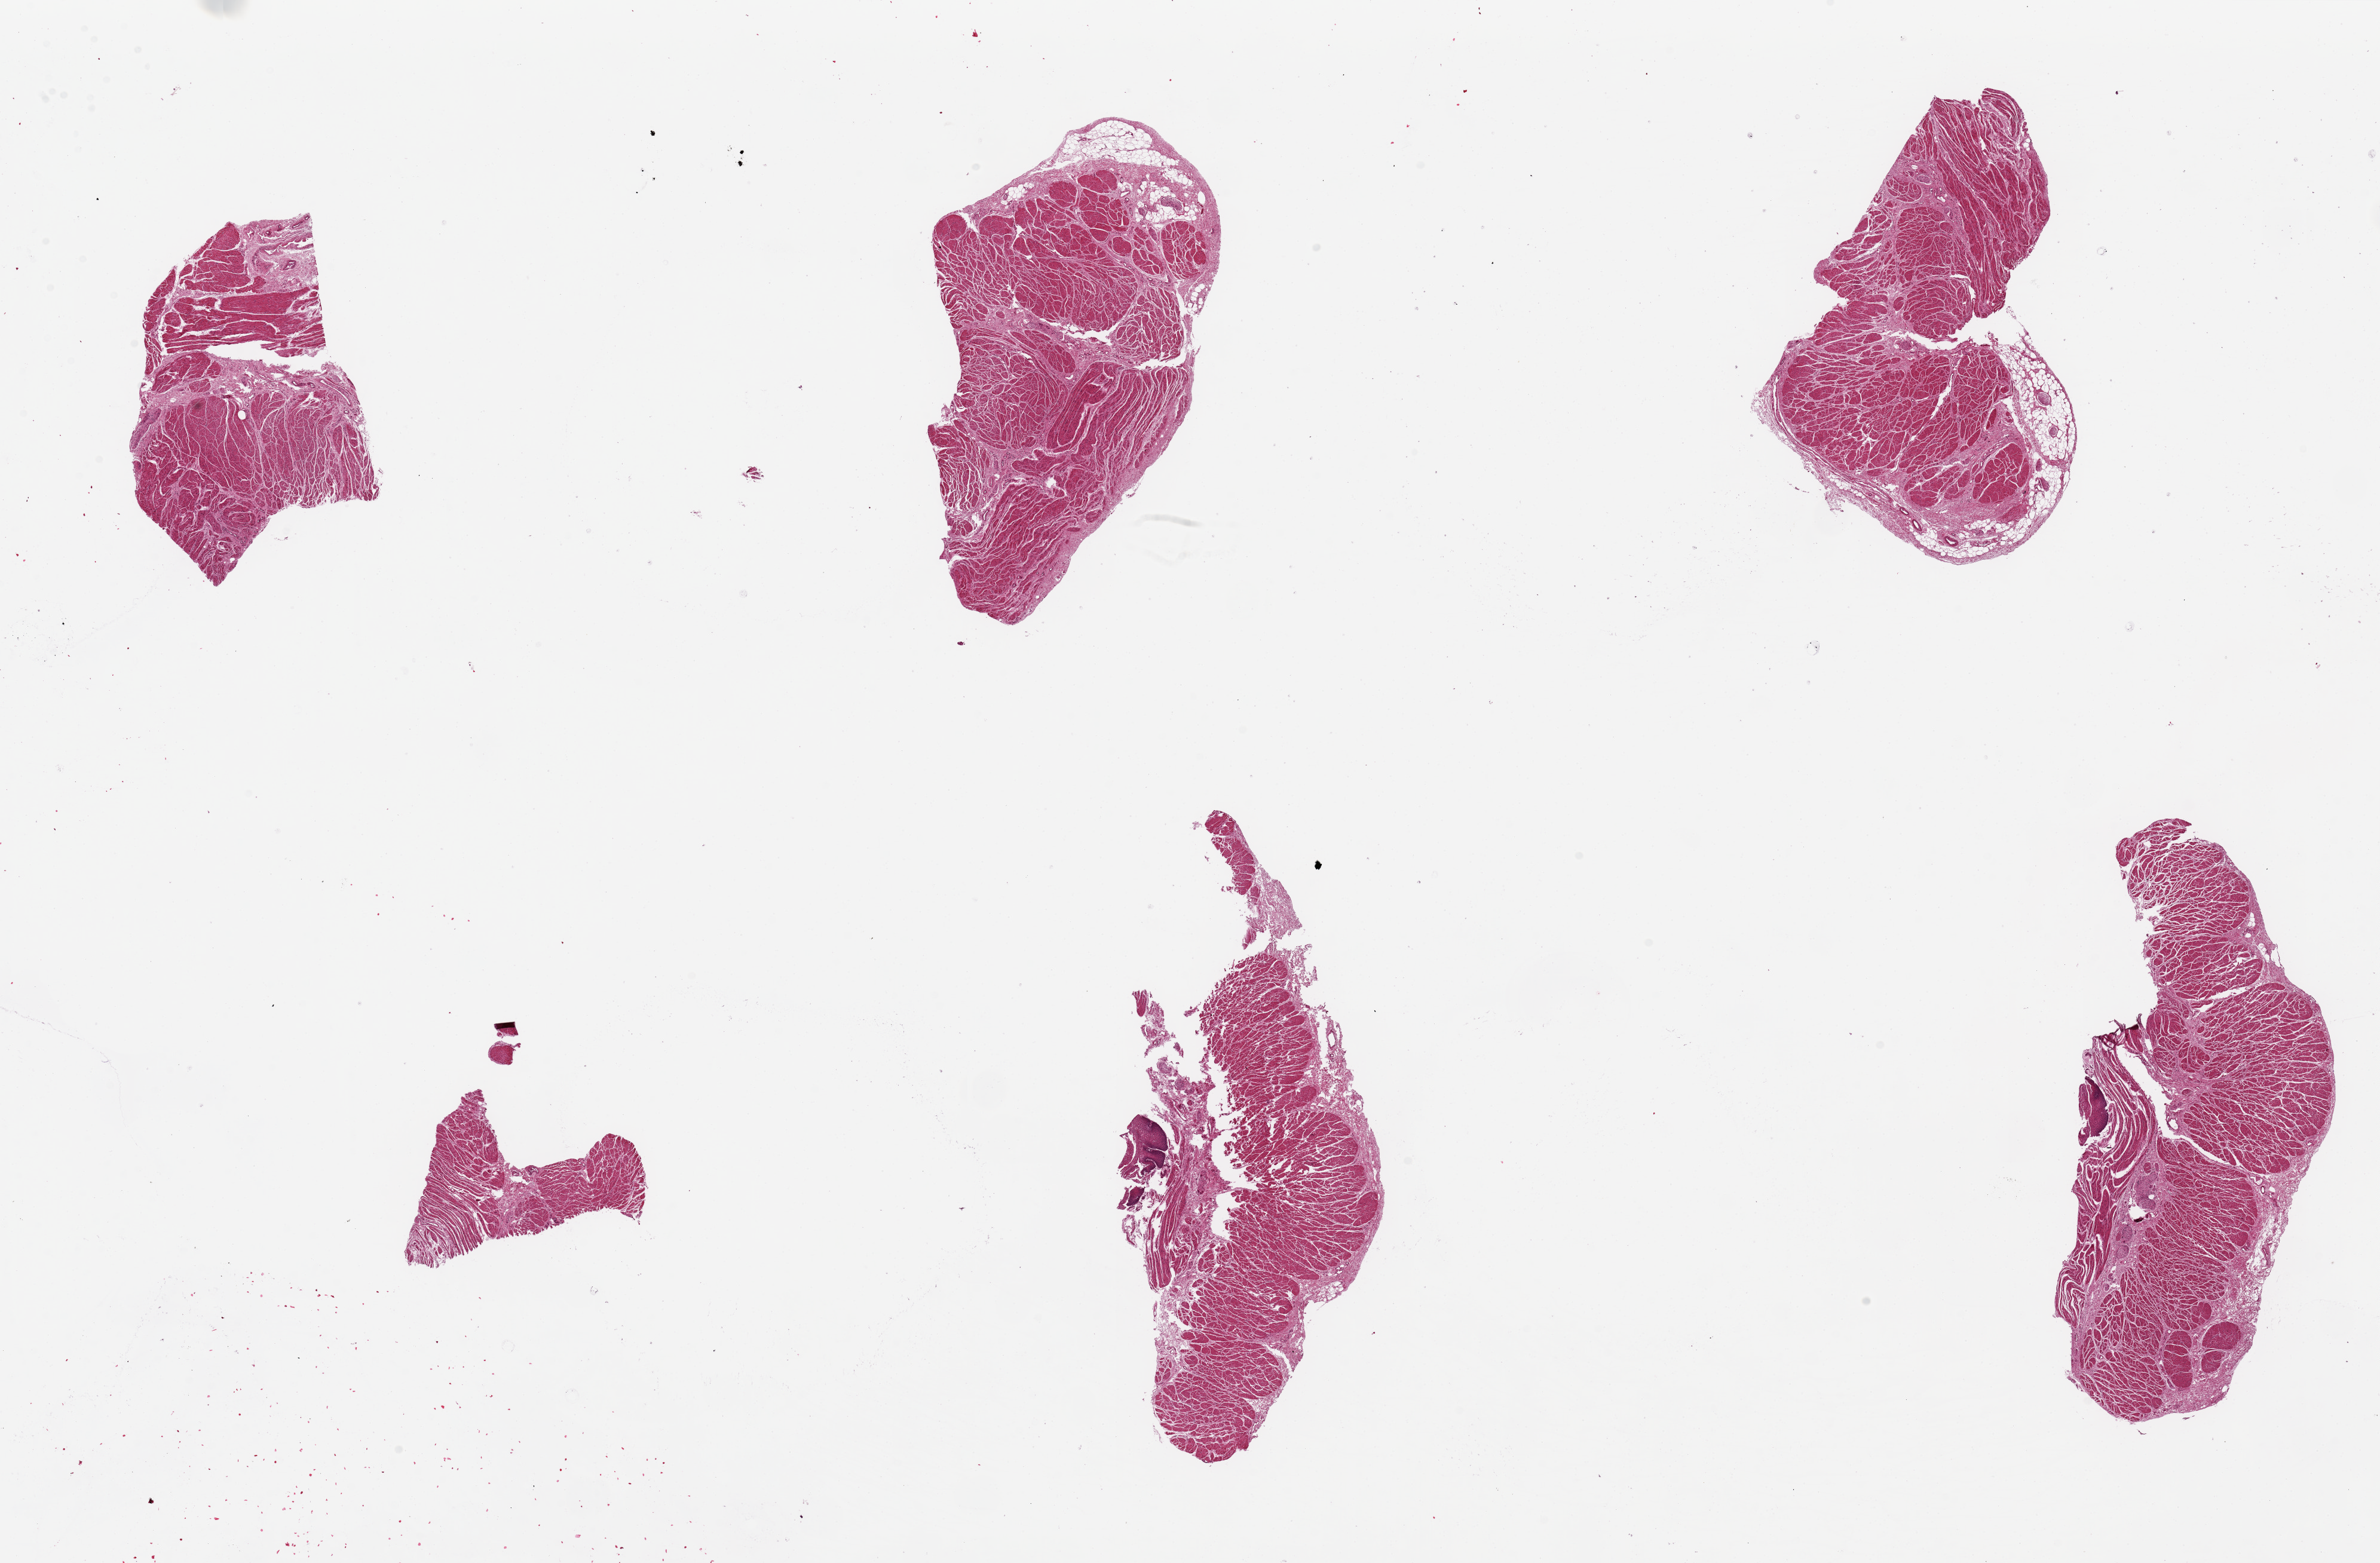
Hematoxylin and eosin (H&E) whole-slide image, brightfield — whole scanned area (about 31.5 x 20.7 mm, acquisition: 20x scan) shown as a low-resolution overview; PAXgene-fixed paraffin-embedded (PFPE) section; sampled site (target tissue): esophageal muscle; tissue donor sample.
Reviewer comment on this tissue sample: 6 pieces, up to 9x3.5mm; all with muscle (target) , 2 with mucosal remnants.